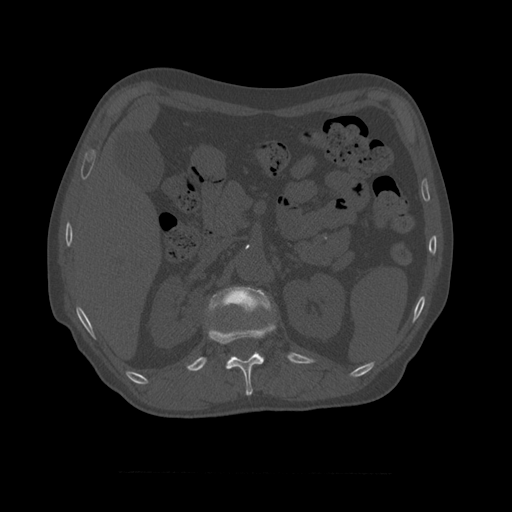
CT including the spine, one axial slice. Slice 372 of 450 in the series (ordered by position). 120 kVp. Bone window (W 1800 / L 400 HU). 1.25 mm slice thickness. 512 × 512 image matrix, field of view 405 × 405 mm. Patient age 75 years. Case-level facts recorded for this patient, not image findings: primary cancer: prostate.
Annotated regions visible in this slice (semi-automatically segmented with operator editing):
- L1 vertebra: bounding box <207,287,273,317> (left, top, right, bottom; pixels)
- T11 vertebra: <208,316,276,396>